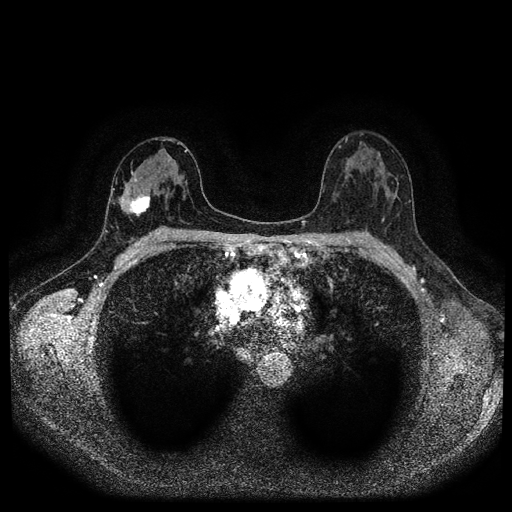
Breast MRI (dynamic contrast-enhanced, multi-phase), one axial slice; slice 60 of 116 in the series (ordered by position); dynamic contrast-enhanced series, time point 2 of 5 at this slice position (early post-contrast); 1.5 T; TE 2.7 ms, TR 5.4 ms; 2 mm slice thickness; 512 × 512 image matrix, field of view 330 × 330 mm. Female patient, age 42 years.
Outlined on this slice (semi-automatic segmentation, software-assisted and operator-edited):
- breast lesion (labelled 'tumour' in the annotation; benign lesions carry a separate 'benign' label): bounding box (x1, y1, x2, y2) in pixels: (127, 194, 151, 219)